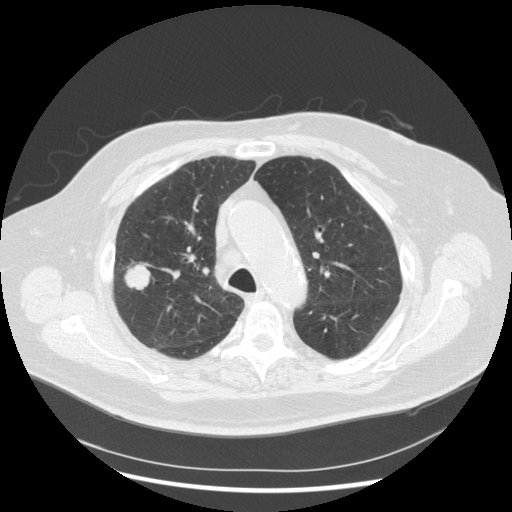
Low-dose screening chest CT, one axial slice. 120 kVp. Lung window (W 1500 / L -600 HU). 2.5 mm slice thickness. 512 × 512 image matrix, field of view 400 × 400 mm.
Structures marked on this image (outlined manually by an expert reader):
- lesion 1 (tumor, upper lobe of right lung): bounding box (x1, y1, x2, y2) in pixels: (125, 264, 150, 290)